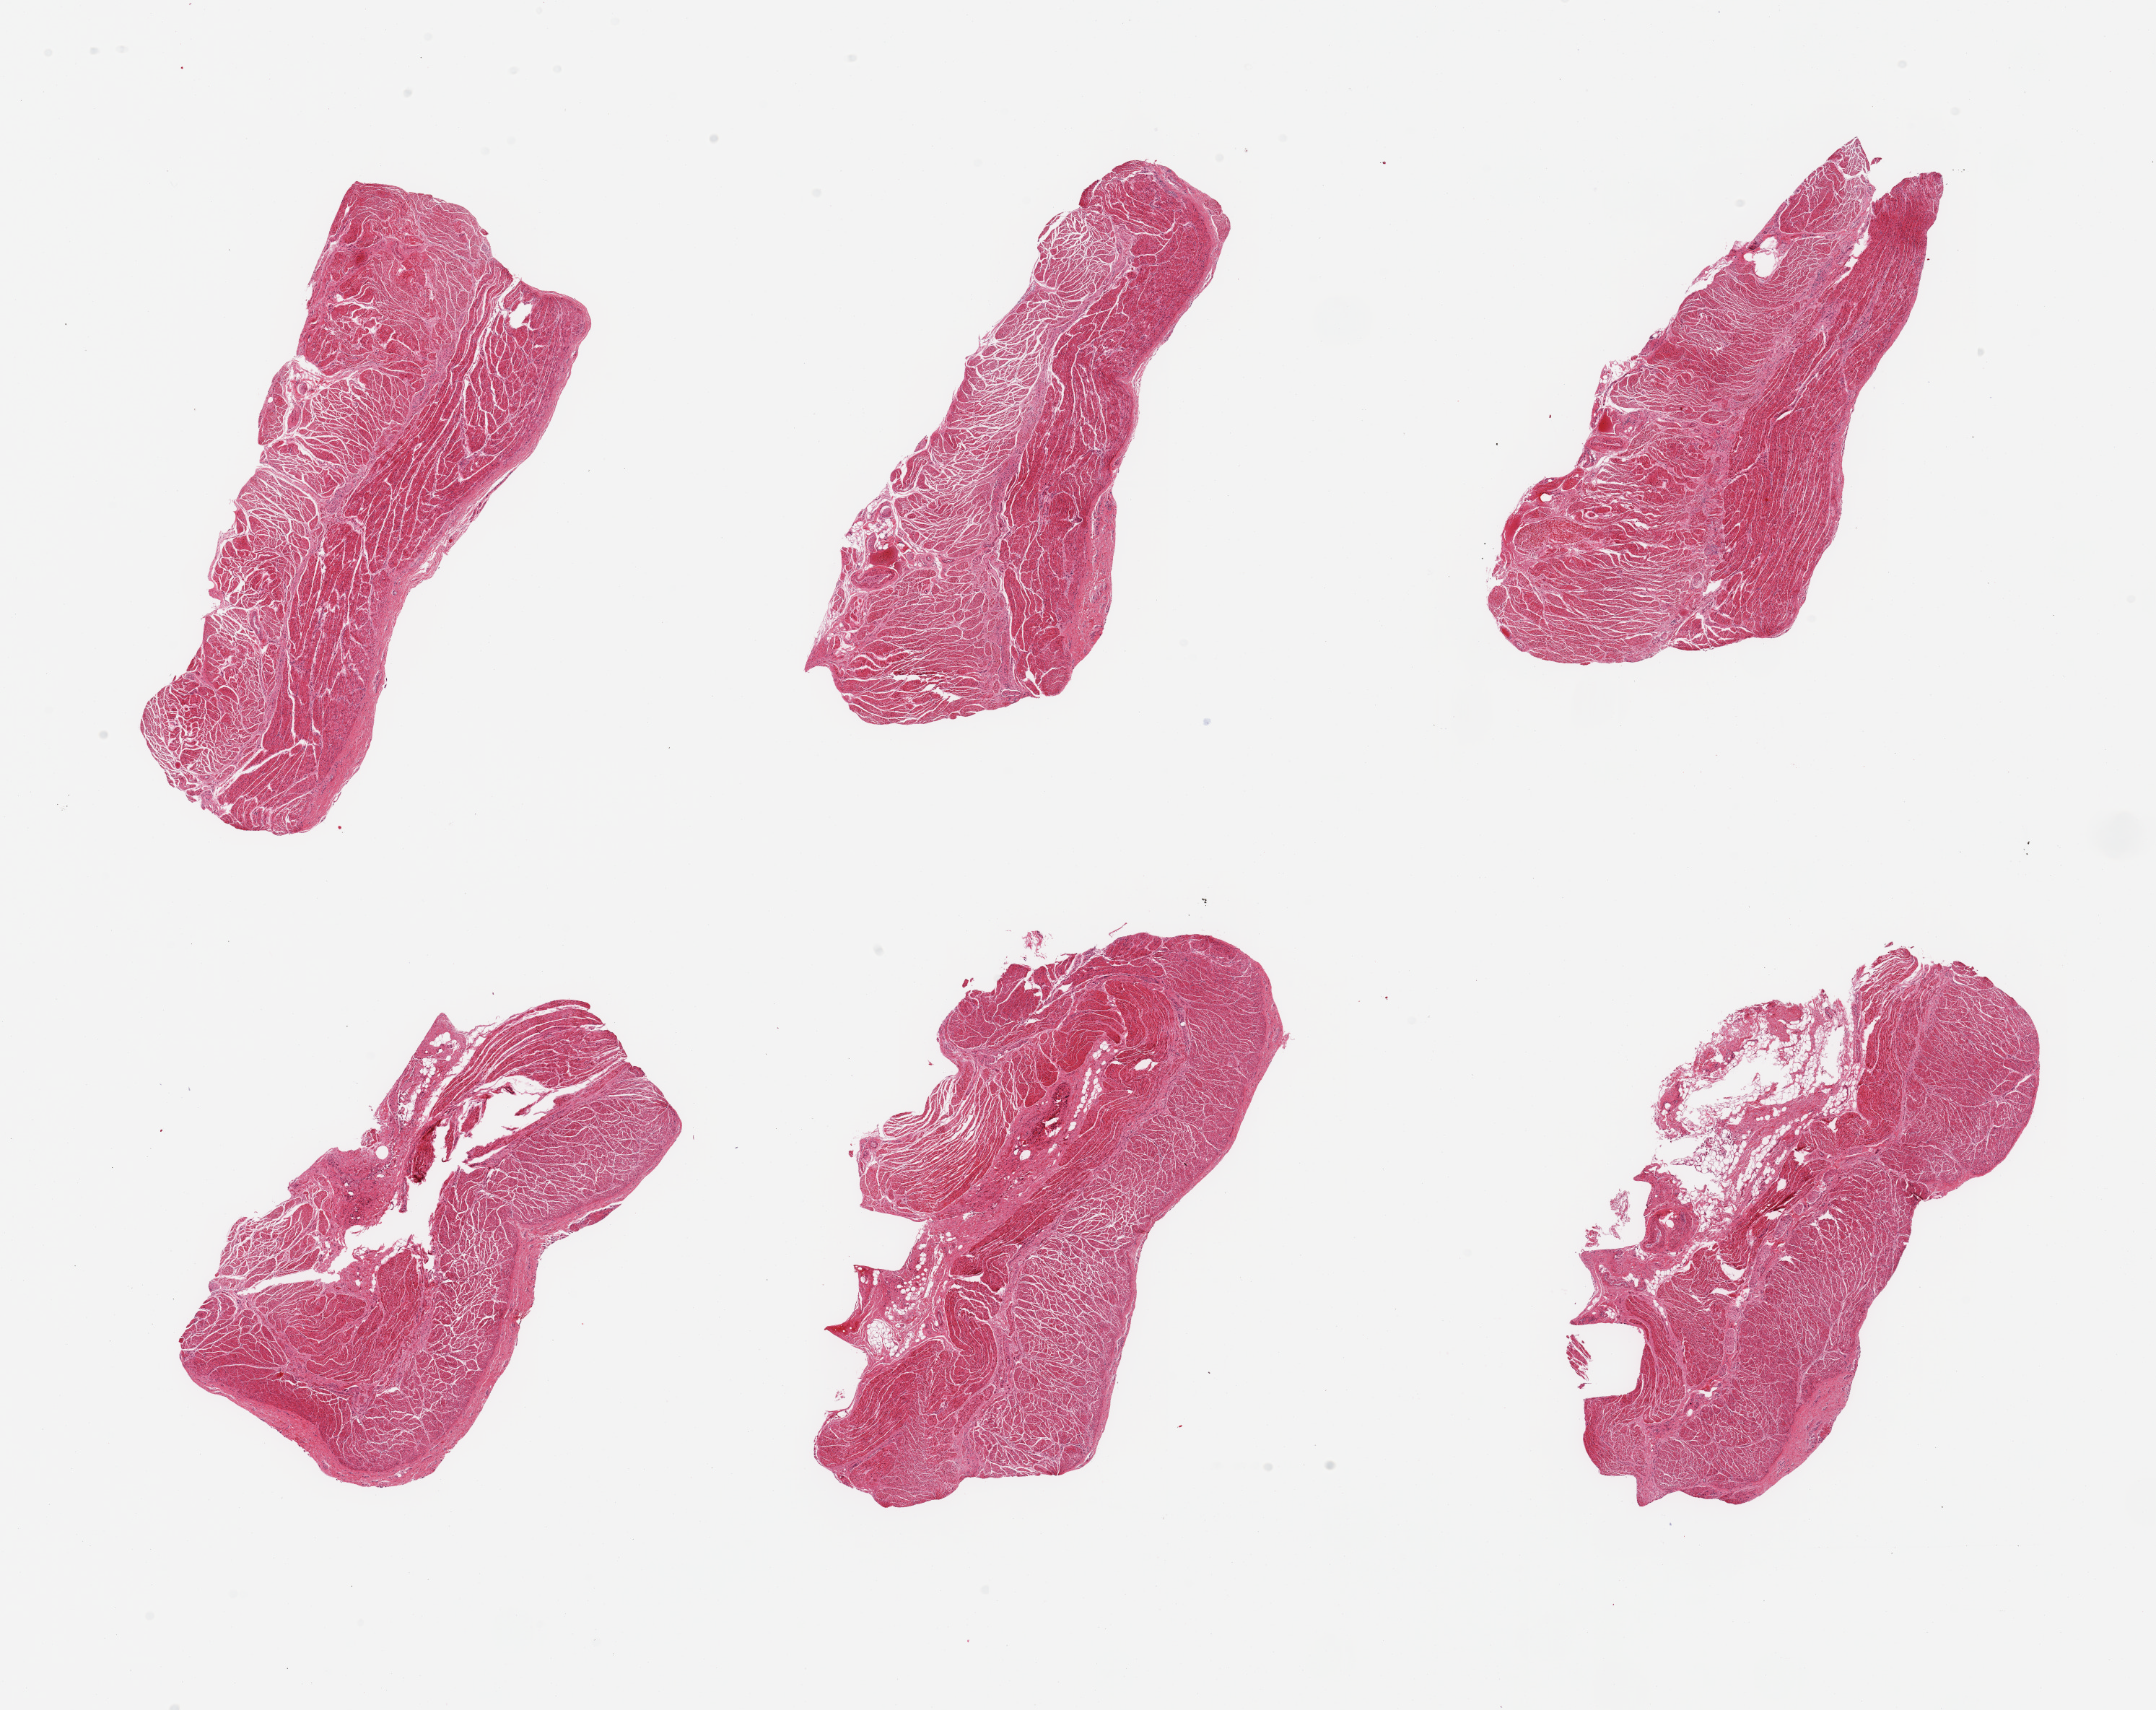
Whole-slide image, H&E stain, a low-resolution overview of the entire scanned area, about 23.6 x 18.7 mm, PAXgene-fixed, paraffin-embedded tissue, target tissue: gastroesophageal junction, donor tissue sample. Female donor.
- reviewer comment on this tissue sample: 6 pieces; muscle fibers fragmented